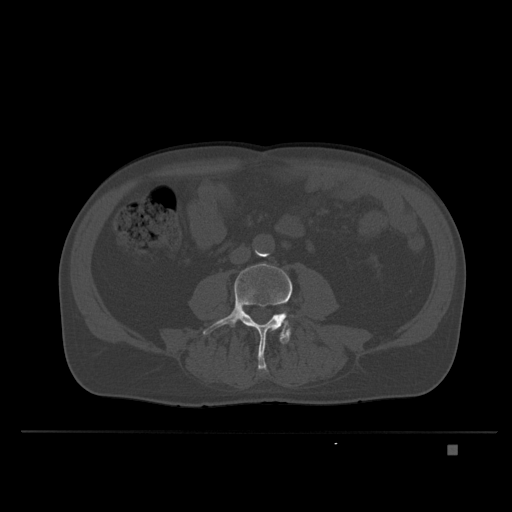
CT including the spine, one axial slice. Position 76 of 435 along the scan axis. Bone window (W 1800 / L 400 HU). 1.5 mm slice thickness. 512 × 512 image matrix, field of view 434 × 434 mm. Male patient, age 73 years. From the clinical record (not read from this slice): primary cancer: skin.
Structures marked on this image (semi-automatic segmentation, software-assisted and operator-edited):
- L4 vertebra: box from (x=202, y=263) to (x=297, y=372) px